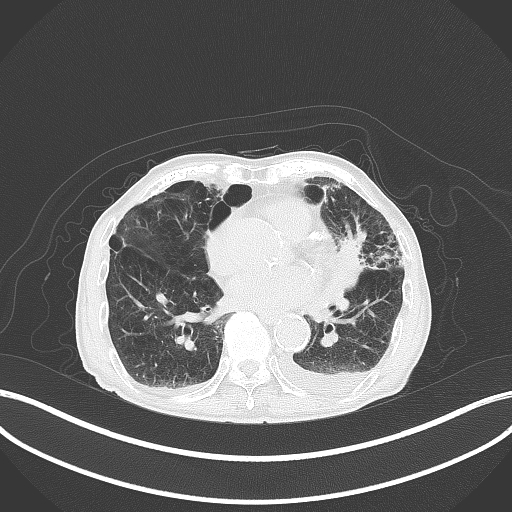
Chest CT, one axial slice. Position 178 of 227 along the scan axis. Reconstruction kernel B70f. Lung window (W 1500 / L -600 HU). 3 mm slice thickness. 512 × 512 image matrix, field of view 400 × 400 mm. Patient: male, 90 years or older. From the clinical record (not read from this slice): clinical TNM (as recorded): T2b N1 M0.
Outlined on this slice (rectangle marked by the reading radiologist):
- lung tumour (recorded histology: squamous cell carcinoma): bounding box <335,231,359,294> (left, top, right, bottom; pixels)